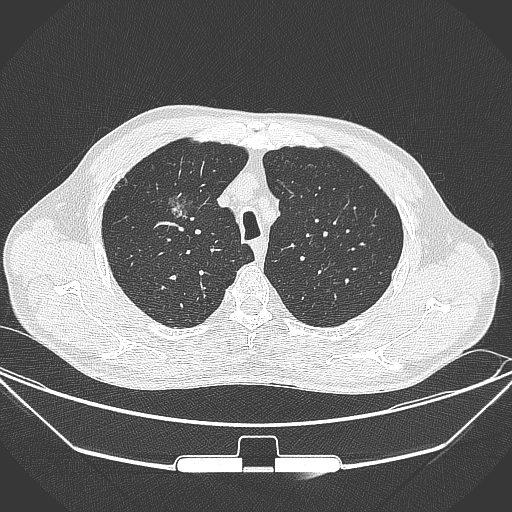
Chest CT, one axial slice. Position 271 of 355 along the scan axis. 120 kVp. Lung window (W 1500 / L -600 HU). 1 mm slice thickness. 512 × 512 image matrix, field of view 399 × 399 mm. Male patient, age 67 years. Case-level facts recorded for this patient, not image findings: clinical TNM (as recorded): T1c N0 M0; histopathological grade: G2.
Annotated regions visible in this slice (rectangle marked by the reading radiologist):
- lung tumour (recorded histology: adenocarcinoma): bounding box <160,188,201,236> (left, top, right, bottom; pixels)